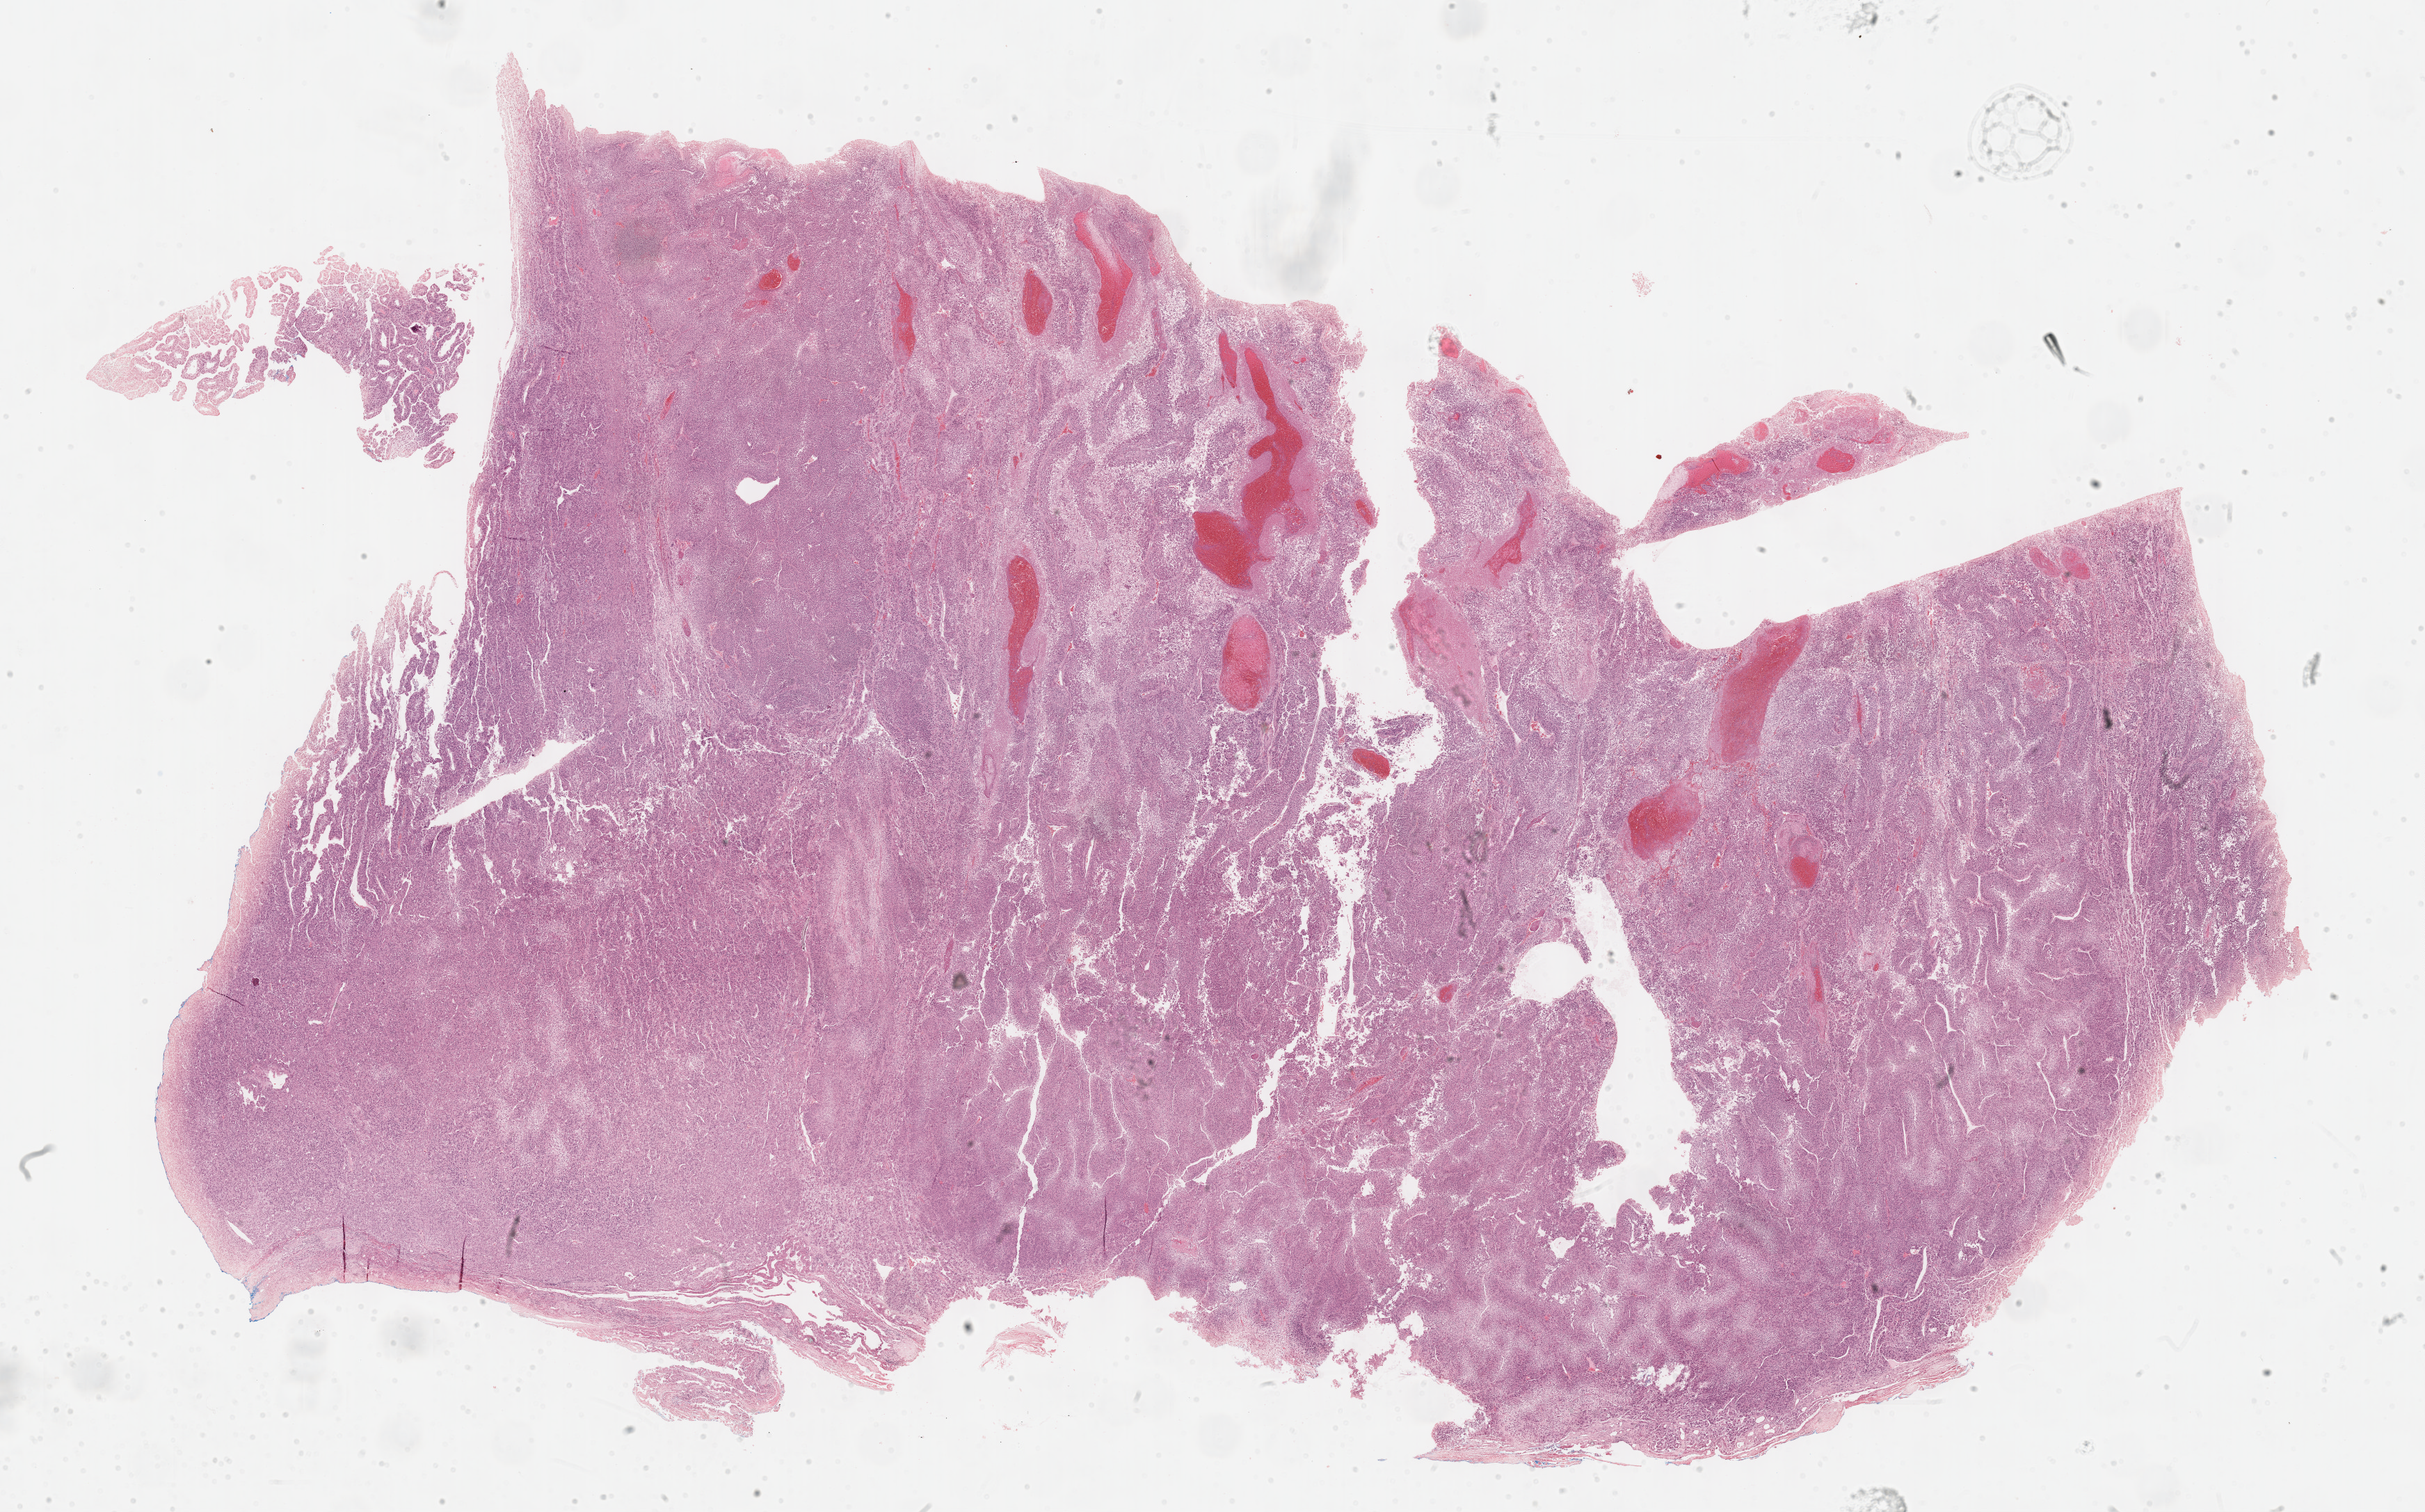
Digitized H&E tissue section (whole slide) — shown as a low-resolution overview of the whole scanned area (about 28.2 x 17.6 mm). Formalin-fixed paraffin-embedded (FFPE) diagnostic section. Primary tumour sample from the adrenal cortex. Female, age 61 years at initial diagnosis.
Histologic diagnosis: Adrenal cortical carcinoma (cortex of adrenal gland).